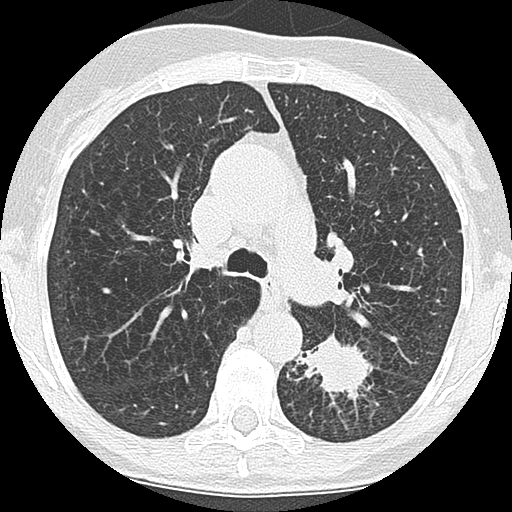
Low-dose screening chest CT, one axial slice. Slice 116 of 171 in the series (ordered by position). 120 kVp. Lung window (W 1500 / L -600 HU). 2.5 mm slice thickness. 512 × 512 image matrix, field of view 280 × 280 mm.
Annotated regions visible in this slice (outlined manually by an expert reader):
- lesion 1 (tumor, lower lobe of left lung): box from (x=294, y=335) to (x=373, y=398) px